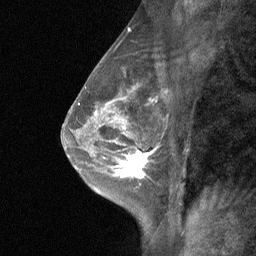
Breast MRI (dynamic contrast-enhanced), one sagittal slice; position 39 of 64 along the scan axis; dynamic contrast-enhanced study with each time point stored as its own series, time point 2 of 3 at this slice position (early post-contrast, ordered by acquisition time); 1.5 T; TE 4.8 ms, TR 27 ms; 2 mm slice thickness; 256 × 256 image matrix, field of view 180 × 180 mm. Female patient, age 47 years. Case-level facts recorded for this patient, not image findings: setting: breast cancer imaged before/during neoadjuvant chemotherapy; receptor status: HR-positive, HER2-negative.
Outlined on this slice (semi-automatic segmentation, software-assisted and operator-edited):
- analysis volume of interest (the breast-tissue region the enhancement analysis was run in; not a lesion): box from (x=104, y=138) to (x=161, y=198) px
- tumour enhancement mask (voxels above the 90 % enhancement threshold inside the analysis volume of interest): (x=114, y=141)–(x=155, y=178)